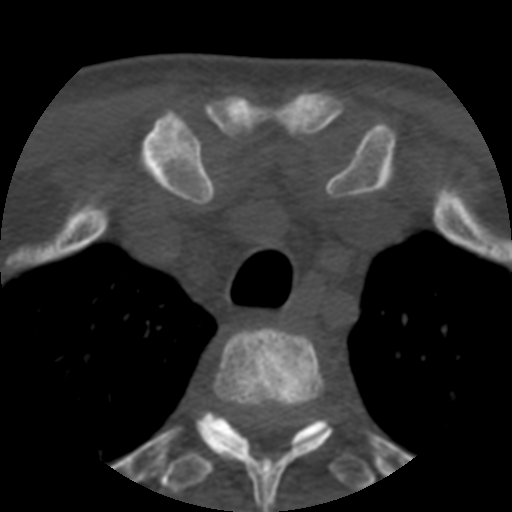
CT including the spine, one axial slice; position 425 of 508 along the scan axis; reconstruction kernel STANDARD; 120 kVp; bone window (W 1800 / L 400 HU); 512 × 512 image matrix. Patient age 57 years. From the clinical record (not read from this slice): primary cancer: prostate.
Outlined on this slice (semi-automatic segmentation, software-assisted and operator-edited):
- T2 vertebra: bounding box (x1, y1, x2, y2) in pixels: (198, 328, 331, 512)
- T3 vertebra: (160, 412, 375, 492)